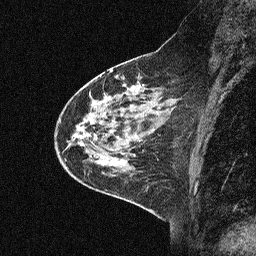
Breast MRI (dynamic contrast-enhanced), one sagittal slice. Slice 22 of 64 in the series (ordered by position). Dynamic contrast-enhanced study with each time point stored as its own series, time point 2 of 3 at this slice position (early post-contrast, ordered by acquisition time). 1.5 T. TE 4.5 ms, TR 11 ms. 2.06 mm slice thickness. 256 × 256 image matrix, field of view 200 × 200 mm. Female patient, age 46 years. From the clinical record (not read from this slice): setting: breast cancer imaged before/during neoadjuvant chemotherapy; receptor status: HER2-positive.
Structures marked on this image (semi-automatic segmentation, software-assisted and operator-edited):
- analysis volume of interest (the breast-tissue region the enhancement analysis was run in; not a lesion): box from (x=46, y=51) to (x=180, y=169) px
- tumour enhancement mask (voxels above the 90 % enhancement threshold inside the analysis volume of interest): (x=91, y=86)–(x=134, y=107)